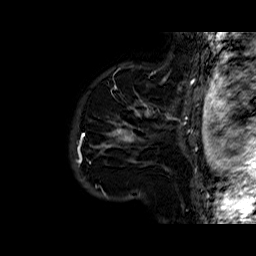
Breast MRI (dynamic contrast-enhanced), one sagittal slice. Position 49 of 60 along the scan axis. Dynamic contrast-enhanced series, time point 2 of 6 at this slice position (early post-contrast). 1.5 T. TE 6.4 ms, TR 32.8 ms. 4 mm slice thickness. 256 × 256 image matrix. Female patient. From the clinical record (not read from this slice): setting: breast cancer imaged before/during neoadjuvant chemotherapy; receptor status: HR-positive, HER2-negative.
Annotated regions visible in this slice (semi-automatic segmentation, software-assisted and operator-edited):
- analysis volume of interest (the breast-tissue region the enhancement analysis was run in; not a lesion): bounding box <87,77,163,167> (left, top, right, bottom; pixels)
- tumour enhancement mask (voxels above the 100 % enhancement threshold inside the analysis volume of interest): <107,103,148,147>